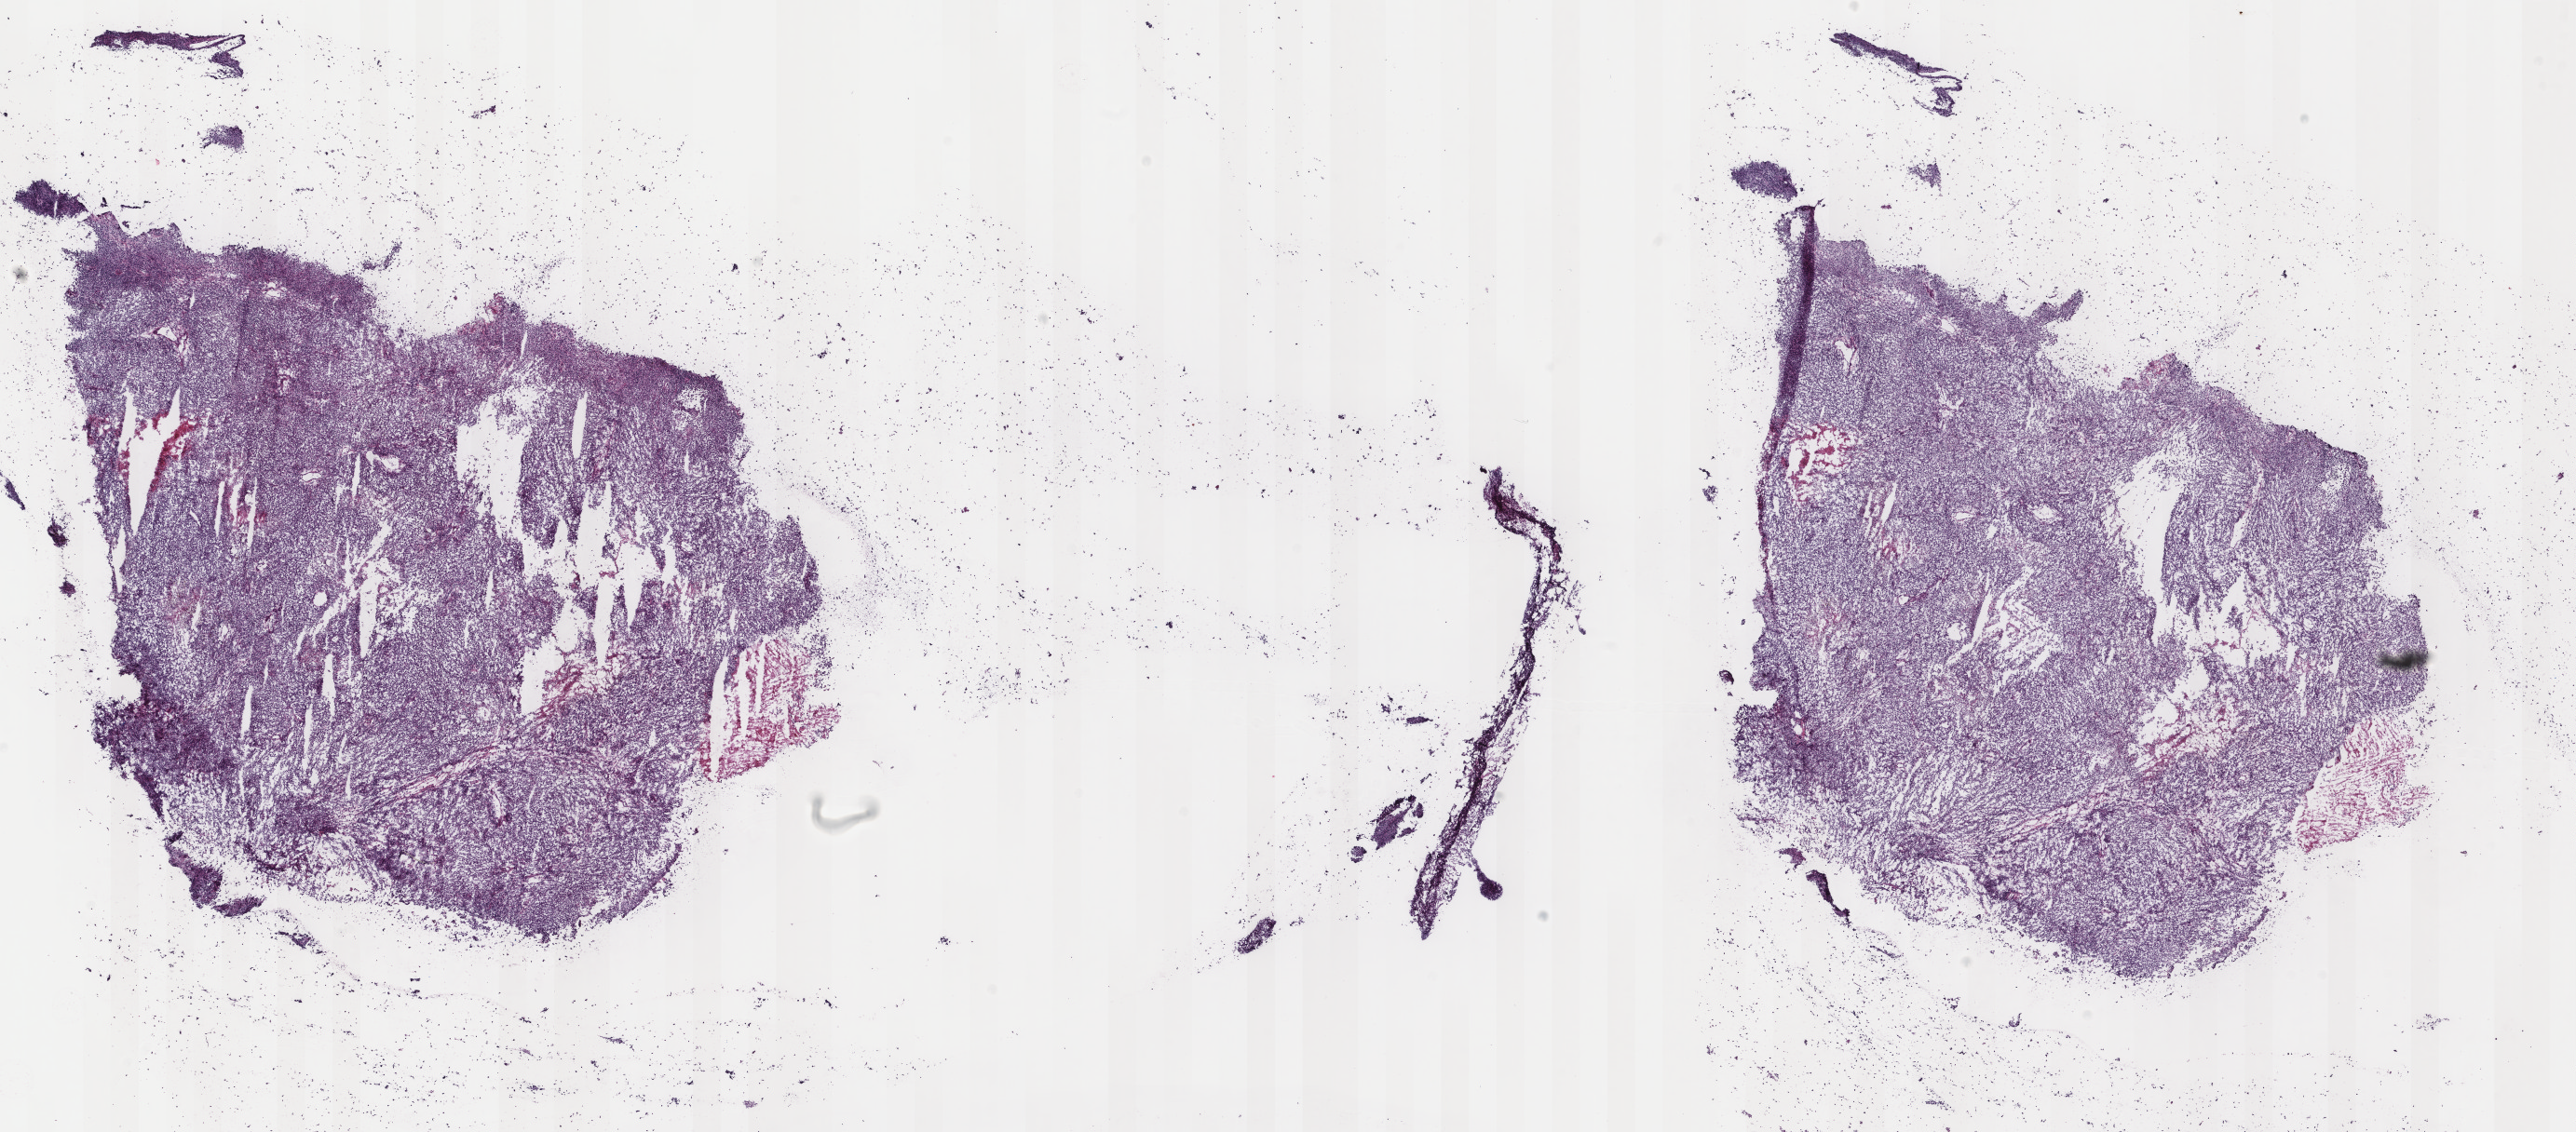
Digitized H&E-stained tissue section (whole slide), shown as a low-resolution overview of the whole scanned area (about 22.0 x 9.7 mm, from a 40x scan). Frozen section. Metastatic tumour sample, sampled site not recorded. Female, age 80 years at initial diagnosis. Pathologist review of this section (percent, as recorded): tumour cells 90%, tumour nuclei 95%, normal cells 0%, stromal cells 0%, necrosis 10%. Inflammatory infiltration, as recorded: lymphocyte infiltration 0%, monocyte infiltration 0%, neutrophil infiltration 0%.
This section: metastatic tumour tissue. Patient diagnosis: Malignant melanoma, NOS.